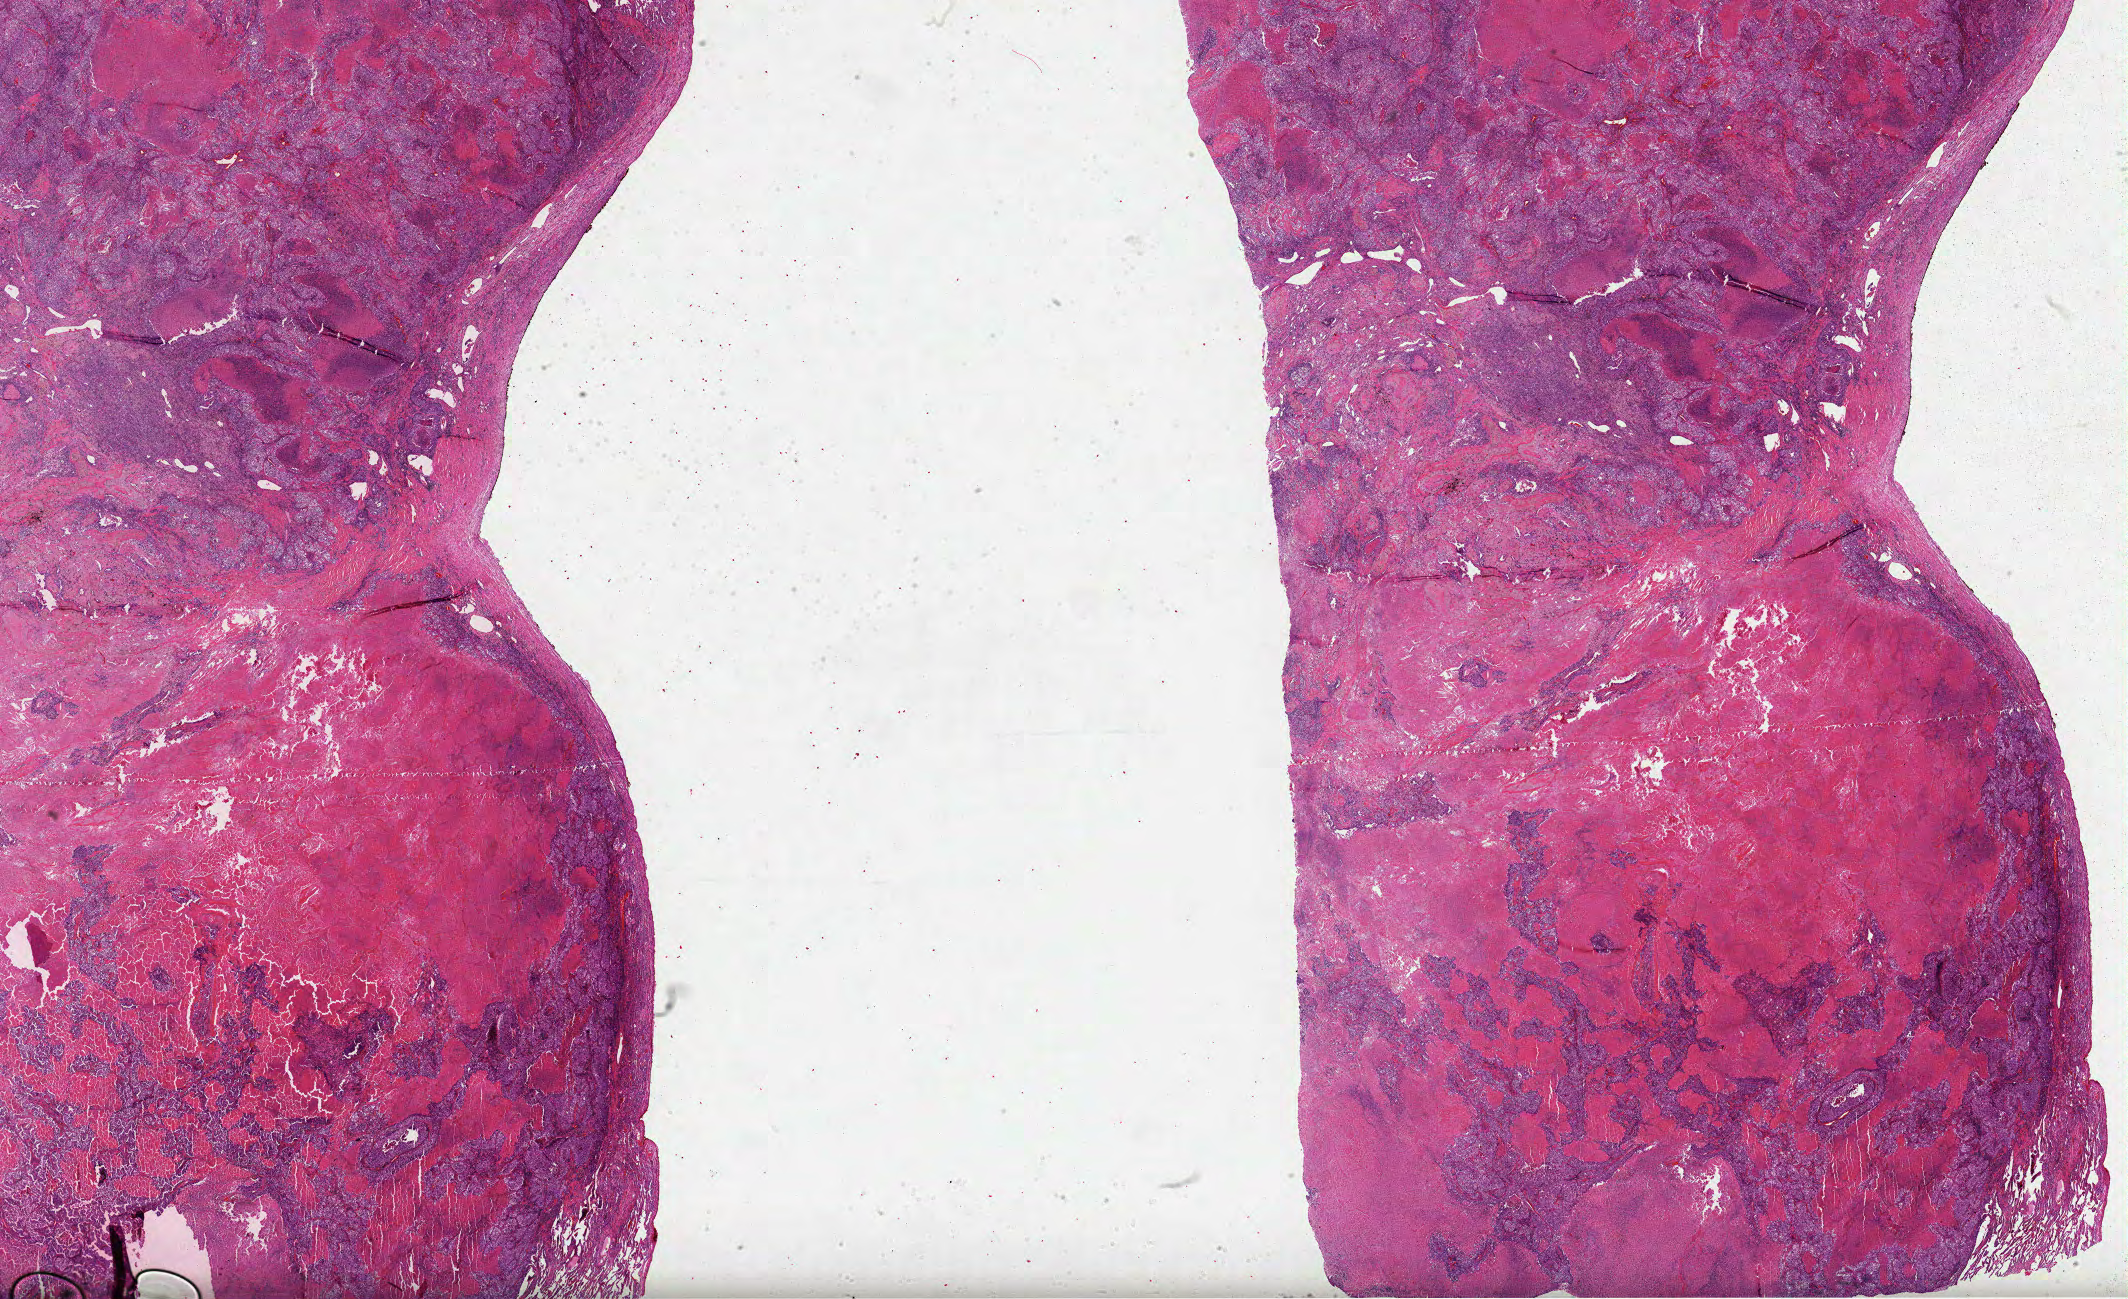
Hematoxylin and eosin (H&E) stained whole-slide image — shown as a low-resolution overview of the whole scanned area (about 34.3 x 21.0 mm, slide scanned at 40x), formalin-fixed paraffin-embedded (FFPE) diagnostic section, lung, primary tumour sample. Female patient; age at initial diagnosis 81 years.
AJCC pathologic stage: IIIA (7th edition). Diagnosis: Clear cell adenocarcinoma, NOS (upper lobe, lung).